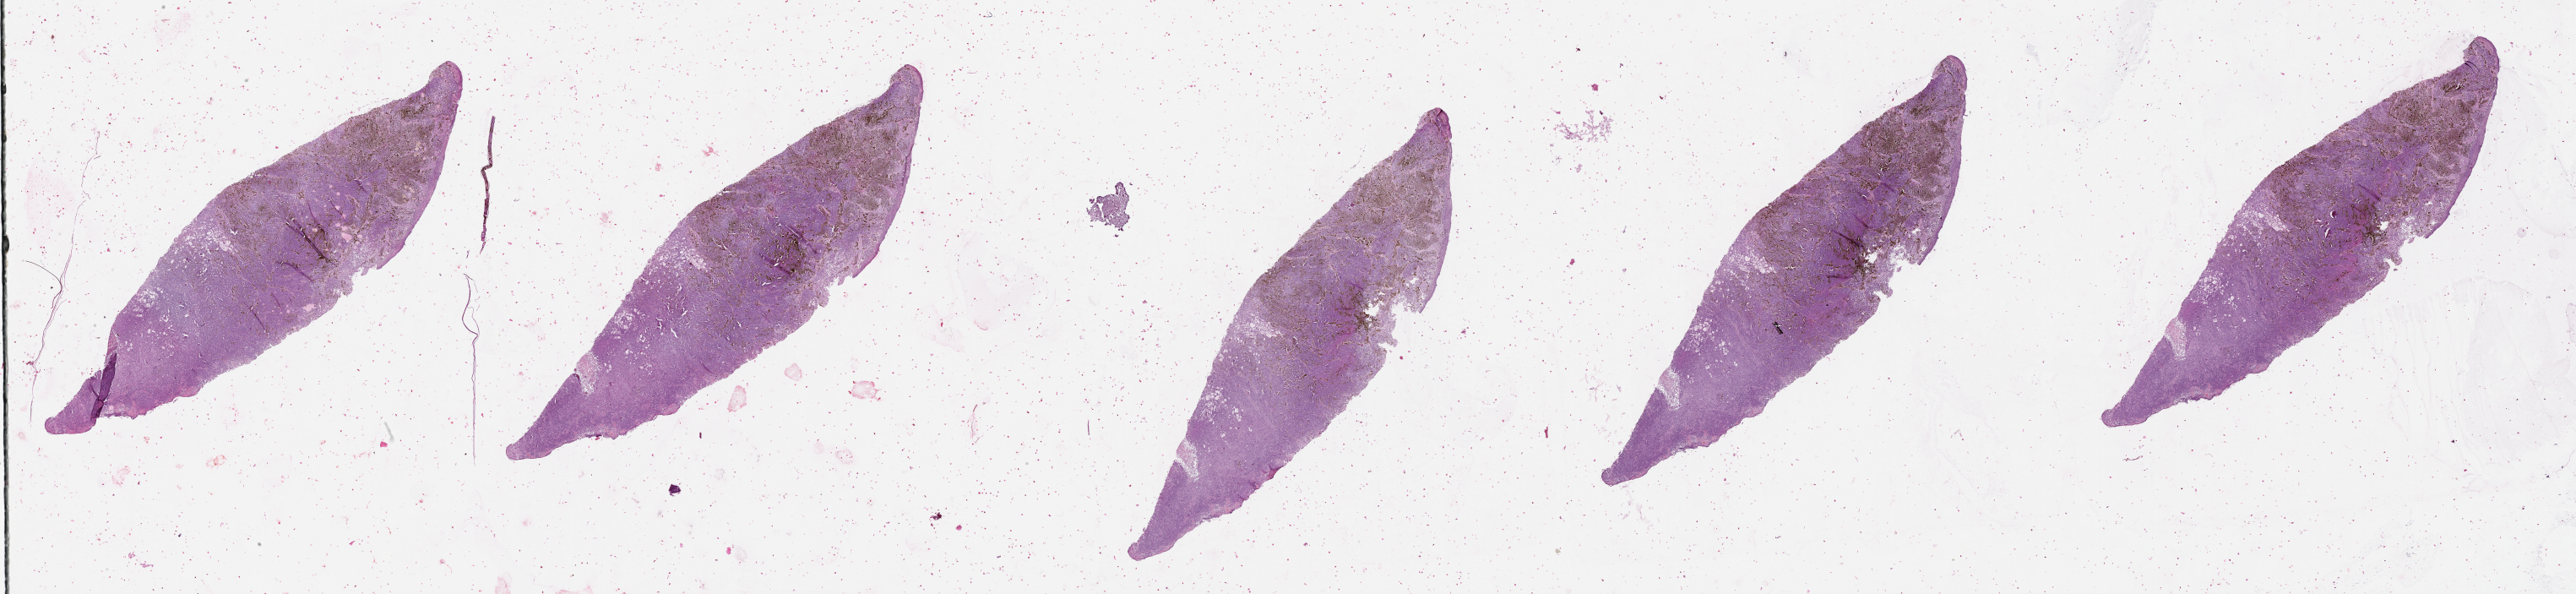
Hematoxylin and eosin (H&E) stained whole-slide image — whole scanned area (about 49.1 x 11.3 mm) shown as a low-resolution overview, tumour tissue sample, sampled site: shoulder. 55-year-old female patient. Pathologist review of this section (percent, as recorded): tumour nuclei 90%, necrosis 5%.
Histologic diagnosis: Malignant melanoma, NOS. AJCC pathologic stage: IIC.